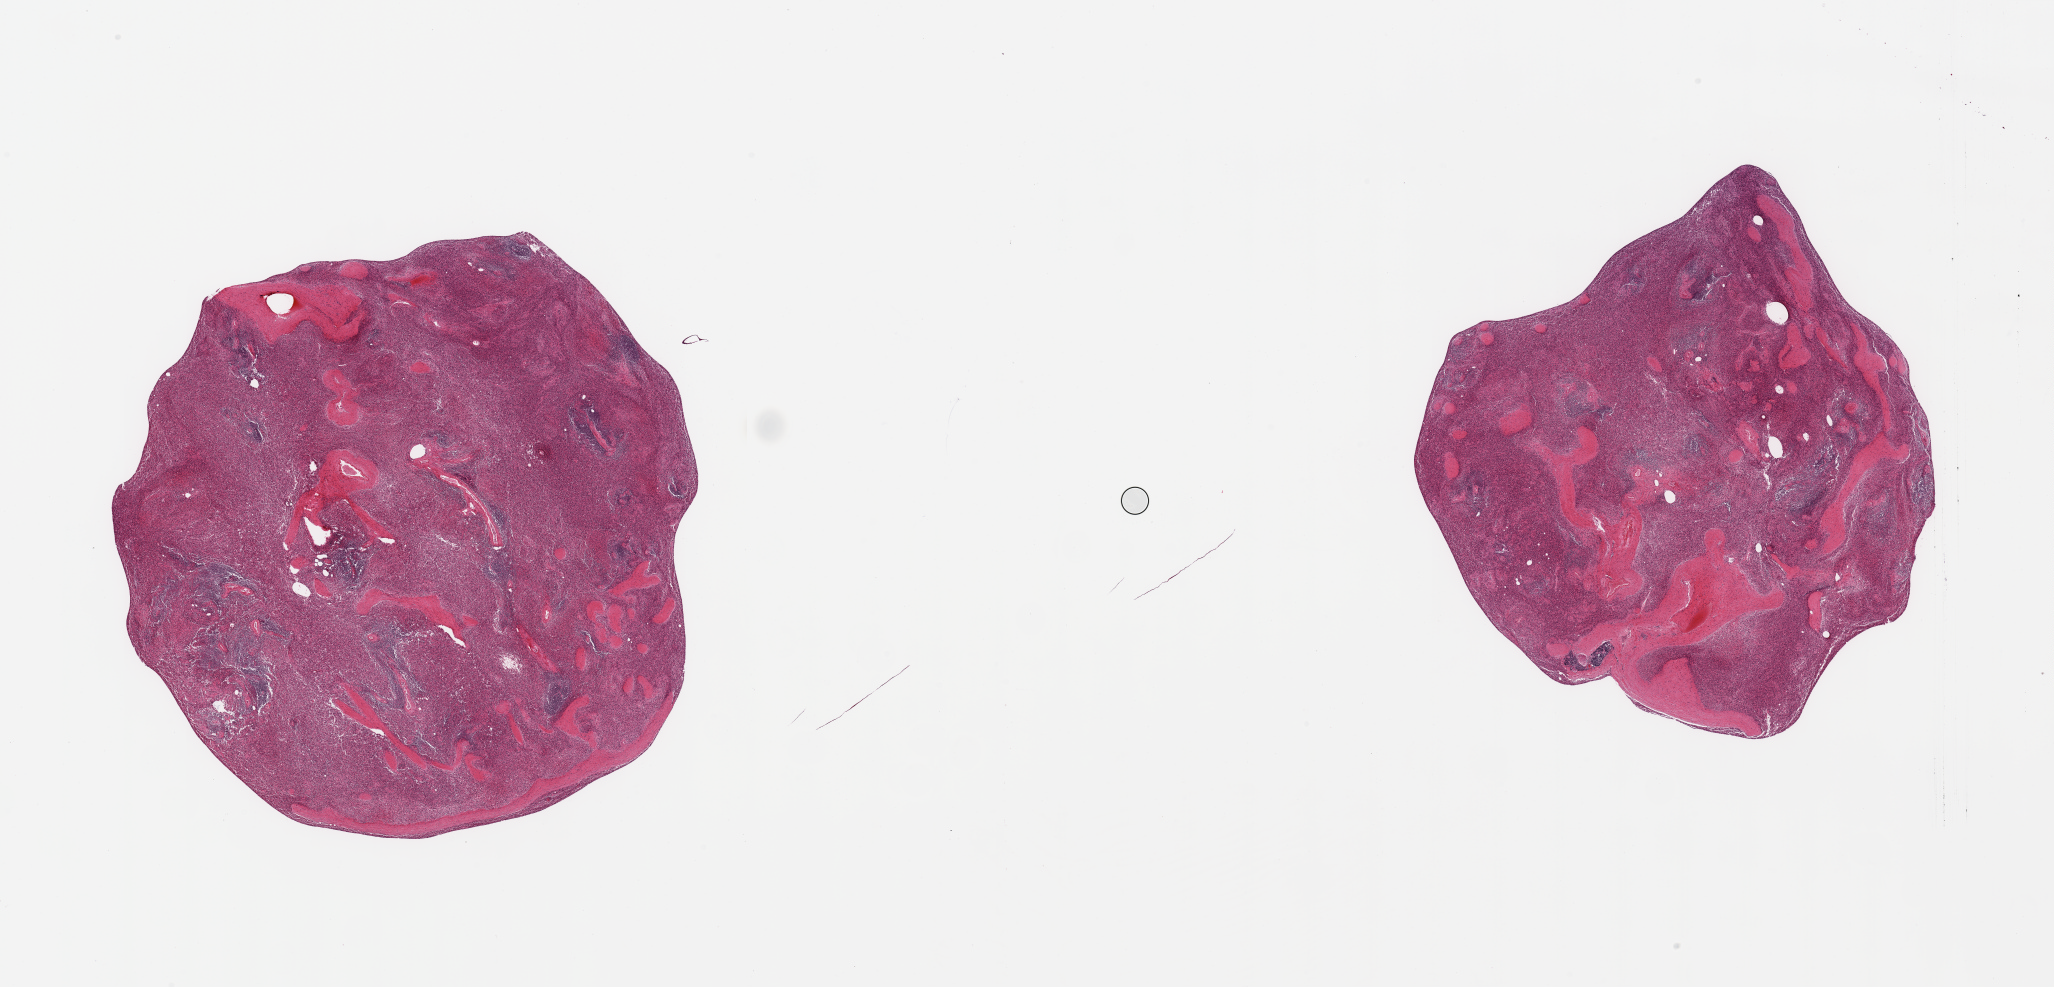
H&E whole-slide image, whole scanned area (about 32.5 x 15.6 mm, from a 20x scan) shown as a low-resolution overview; PAXgene-fixed paraffin-embedded (PFPE) section; sampled site (target tissue): spleen; tissue donor sample.
Pathologist's review note for this sample: 2 pieces; not heavily congested; prominent fibrous septae in 1.